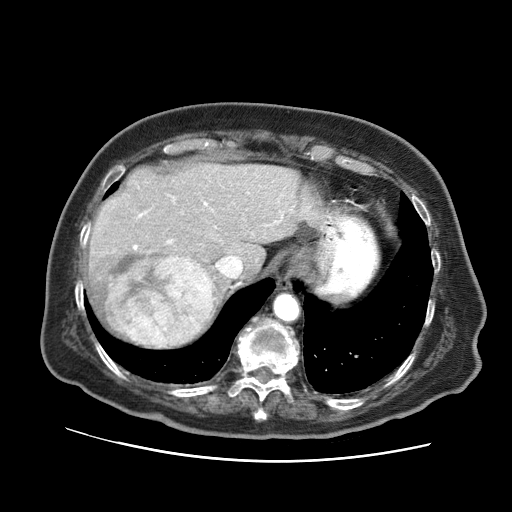
Contrast-enhanced abdominal CT (liver protocol), one axial slice. Slice 53 of 73 in the series (ordered by position). 120 kVp. Soft-tissue window (W 400 / L 40 HU). 512 × 512 image matrix, field of view 380 × 380 mm. From the clinical record (not read from this slice): diagnosis: hepatocellular carcinoma (patient treated with transarterial chemoembolisation; whether this scan precedes or follows treatment is not stated here); TNM stage (as recorded): Stage-I; Child-Pugh class: A; tumour differentiation: well differentiated.
Annotated regions visible in this slice (semi-automatically segmented with operator editing):
- liver parenchyma outside the tumour (the mass and vessels are separate outlines, so this box may not span the whole liver): bounding box <87,164,302,349> (left, top, right, bottom; pixels)
- mass: <104,249,214,348>
- liver vessels: <133,202,284,250>